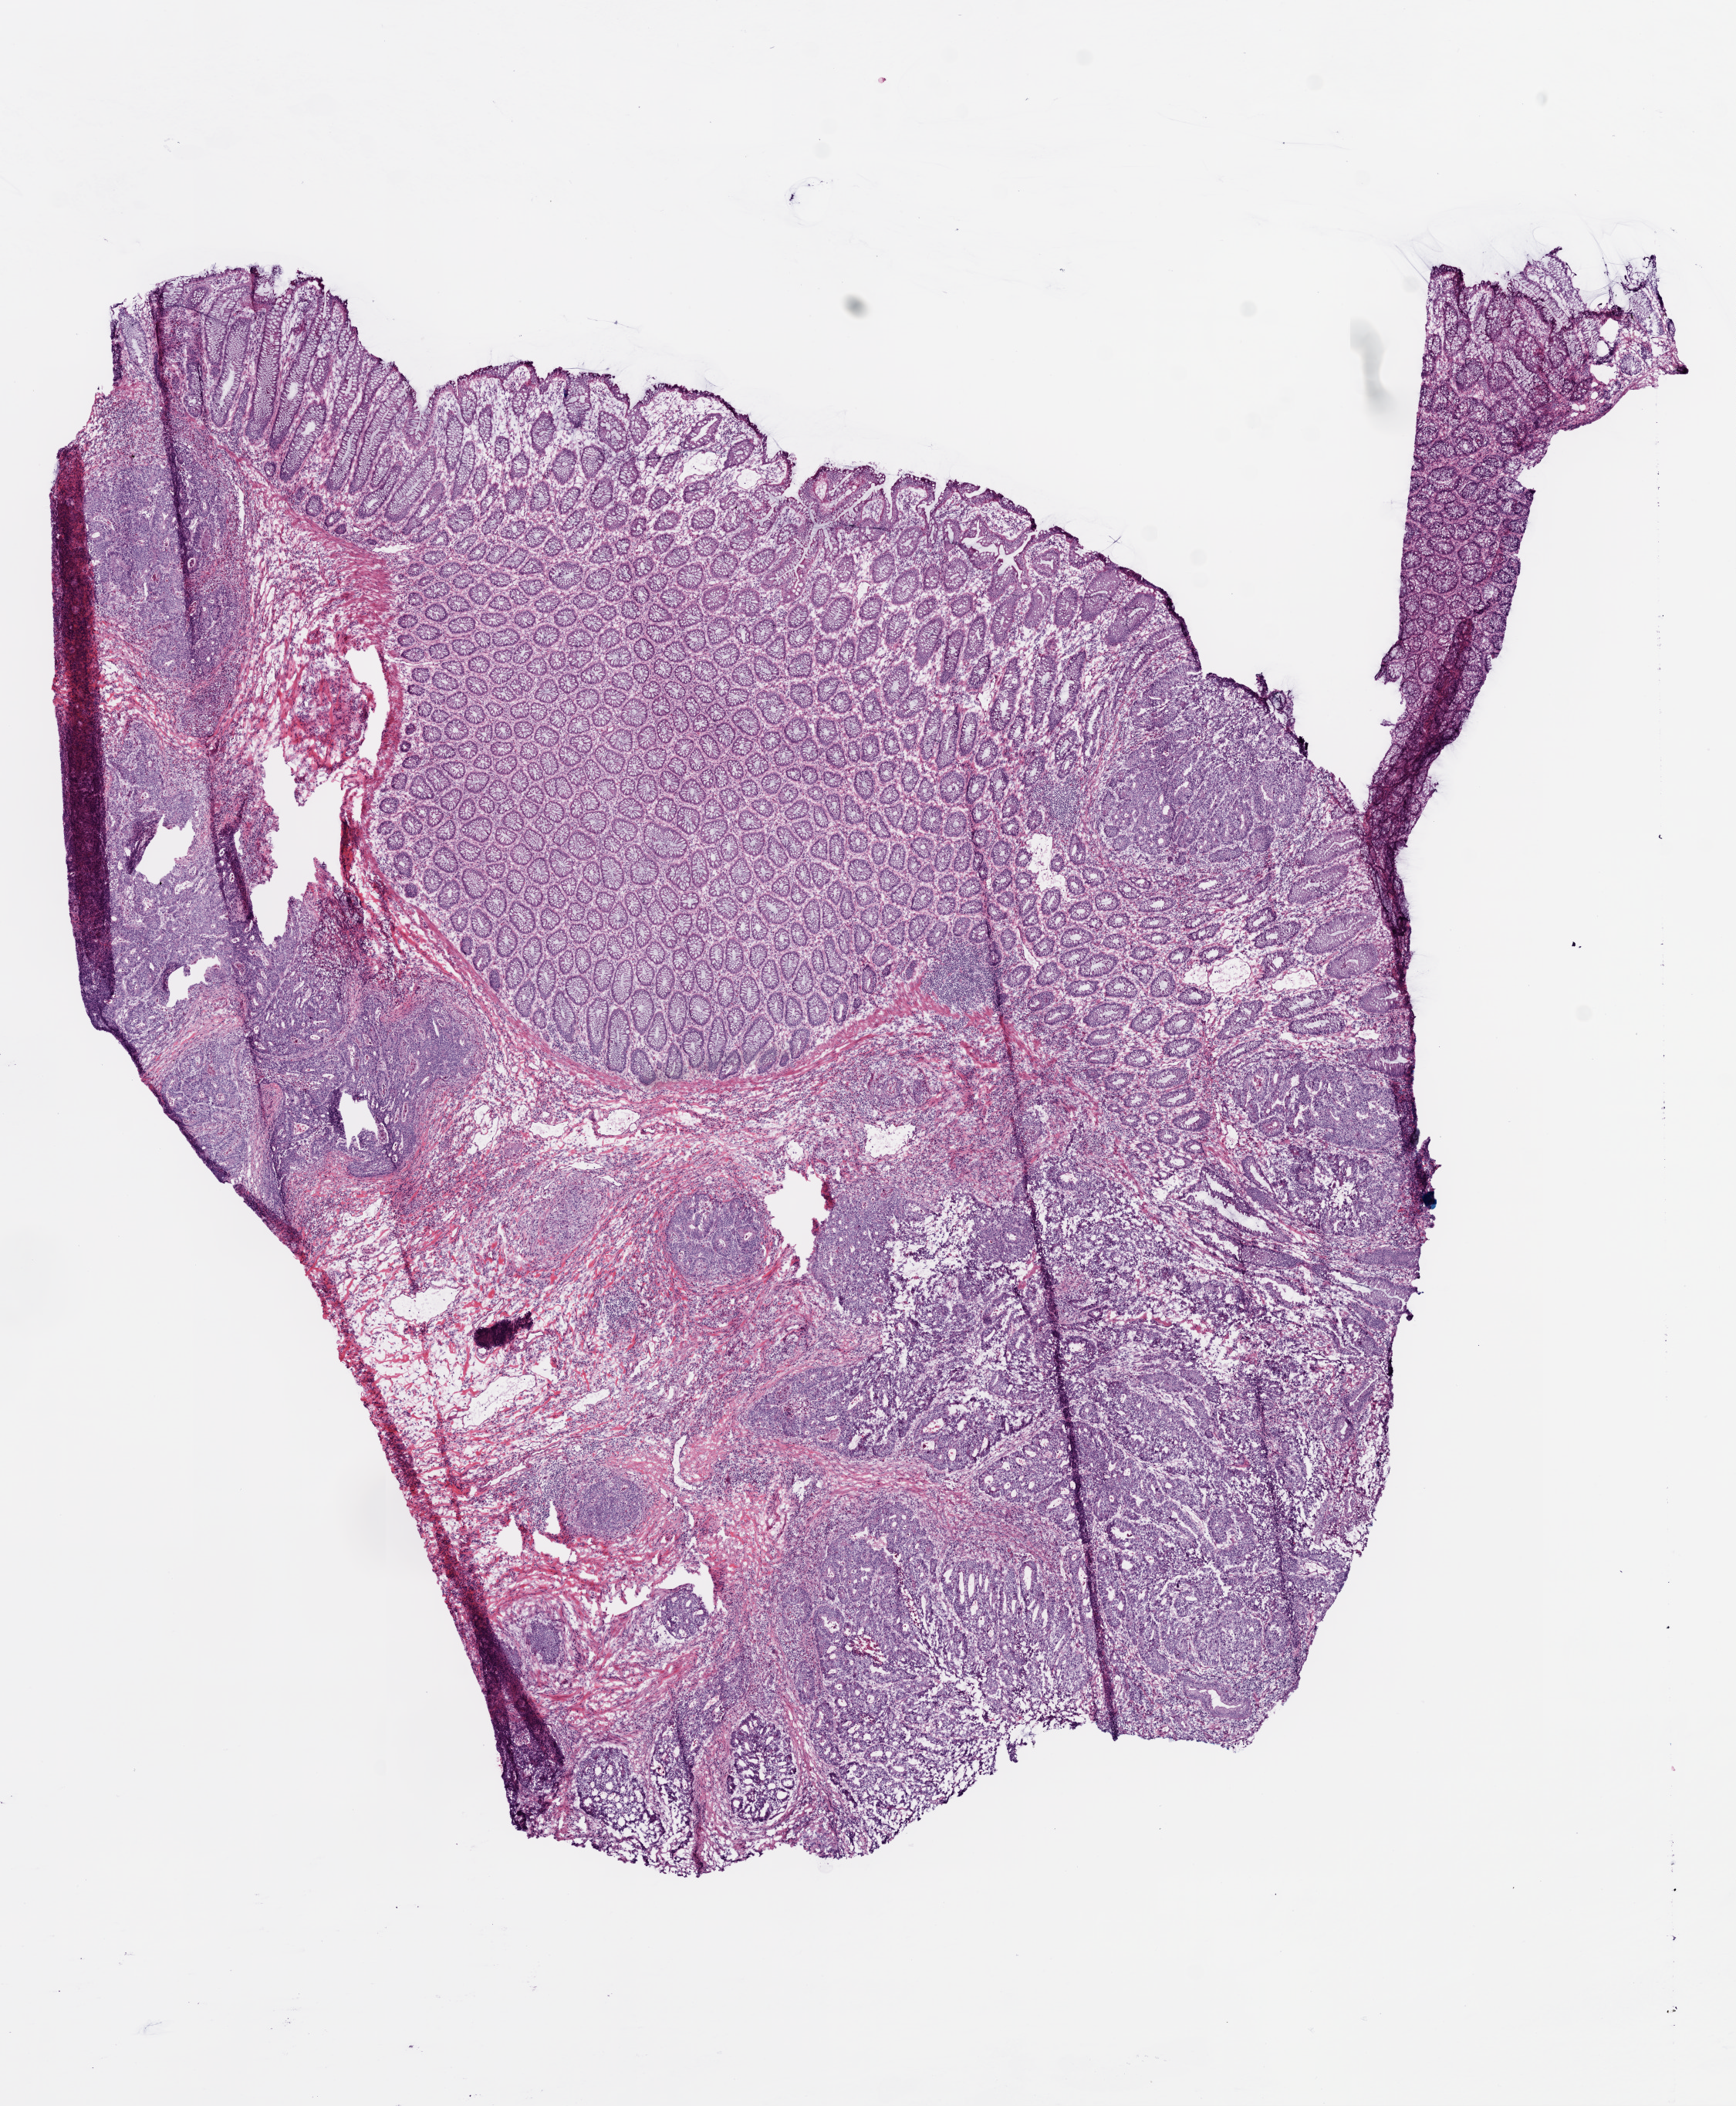
Digitized H&E tissue section (whole slide) — a low-resolution overview of the entire scanned area, about 9.0 x 10.9 mm (slide scanned at 20x). Frozen section from the bottom of the tissue portion. Sample: primary tumour, colon. Patient: male, age at initial diagnosis 58 years. Composition of this section per pathologist review: tumour cells 80%, tumour nuclei 90%, normal cells 0%, stromal cells 15%, necrosis 5%.
- diagnosis: Adenocarcinoma, NOS
- AJCC pathologic stage: III (5th edition)
- TNM: T3 N1 M0